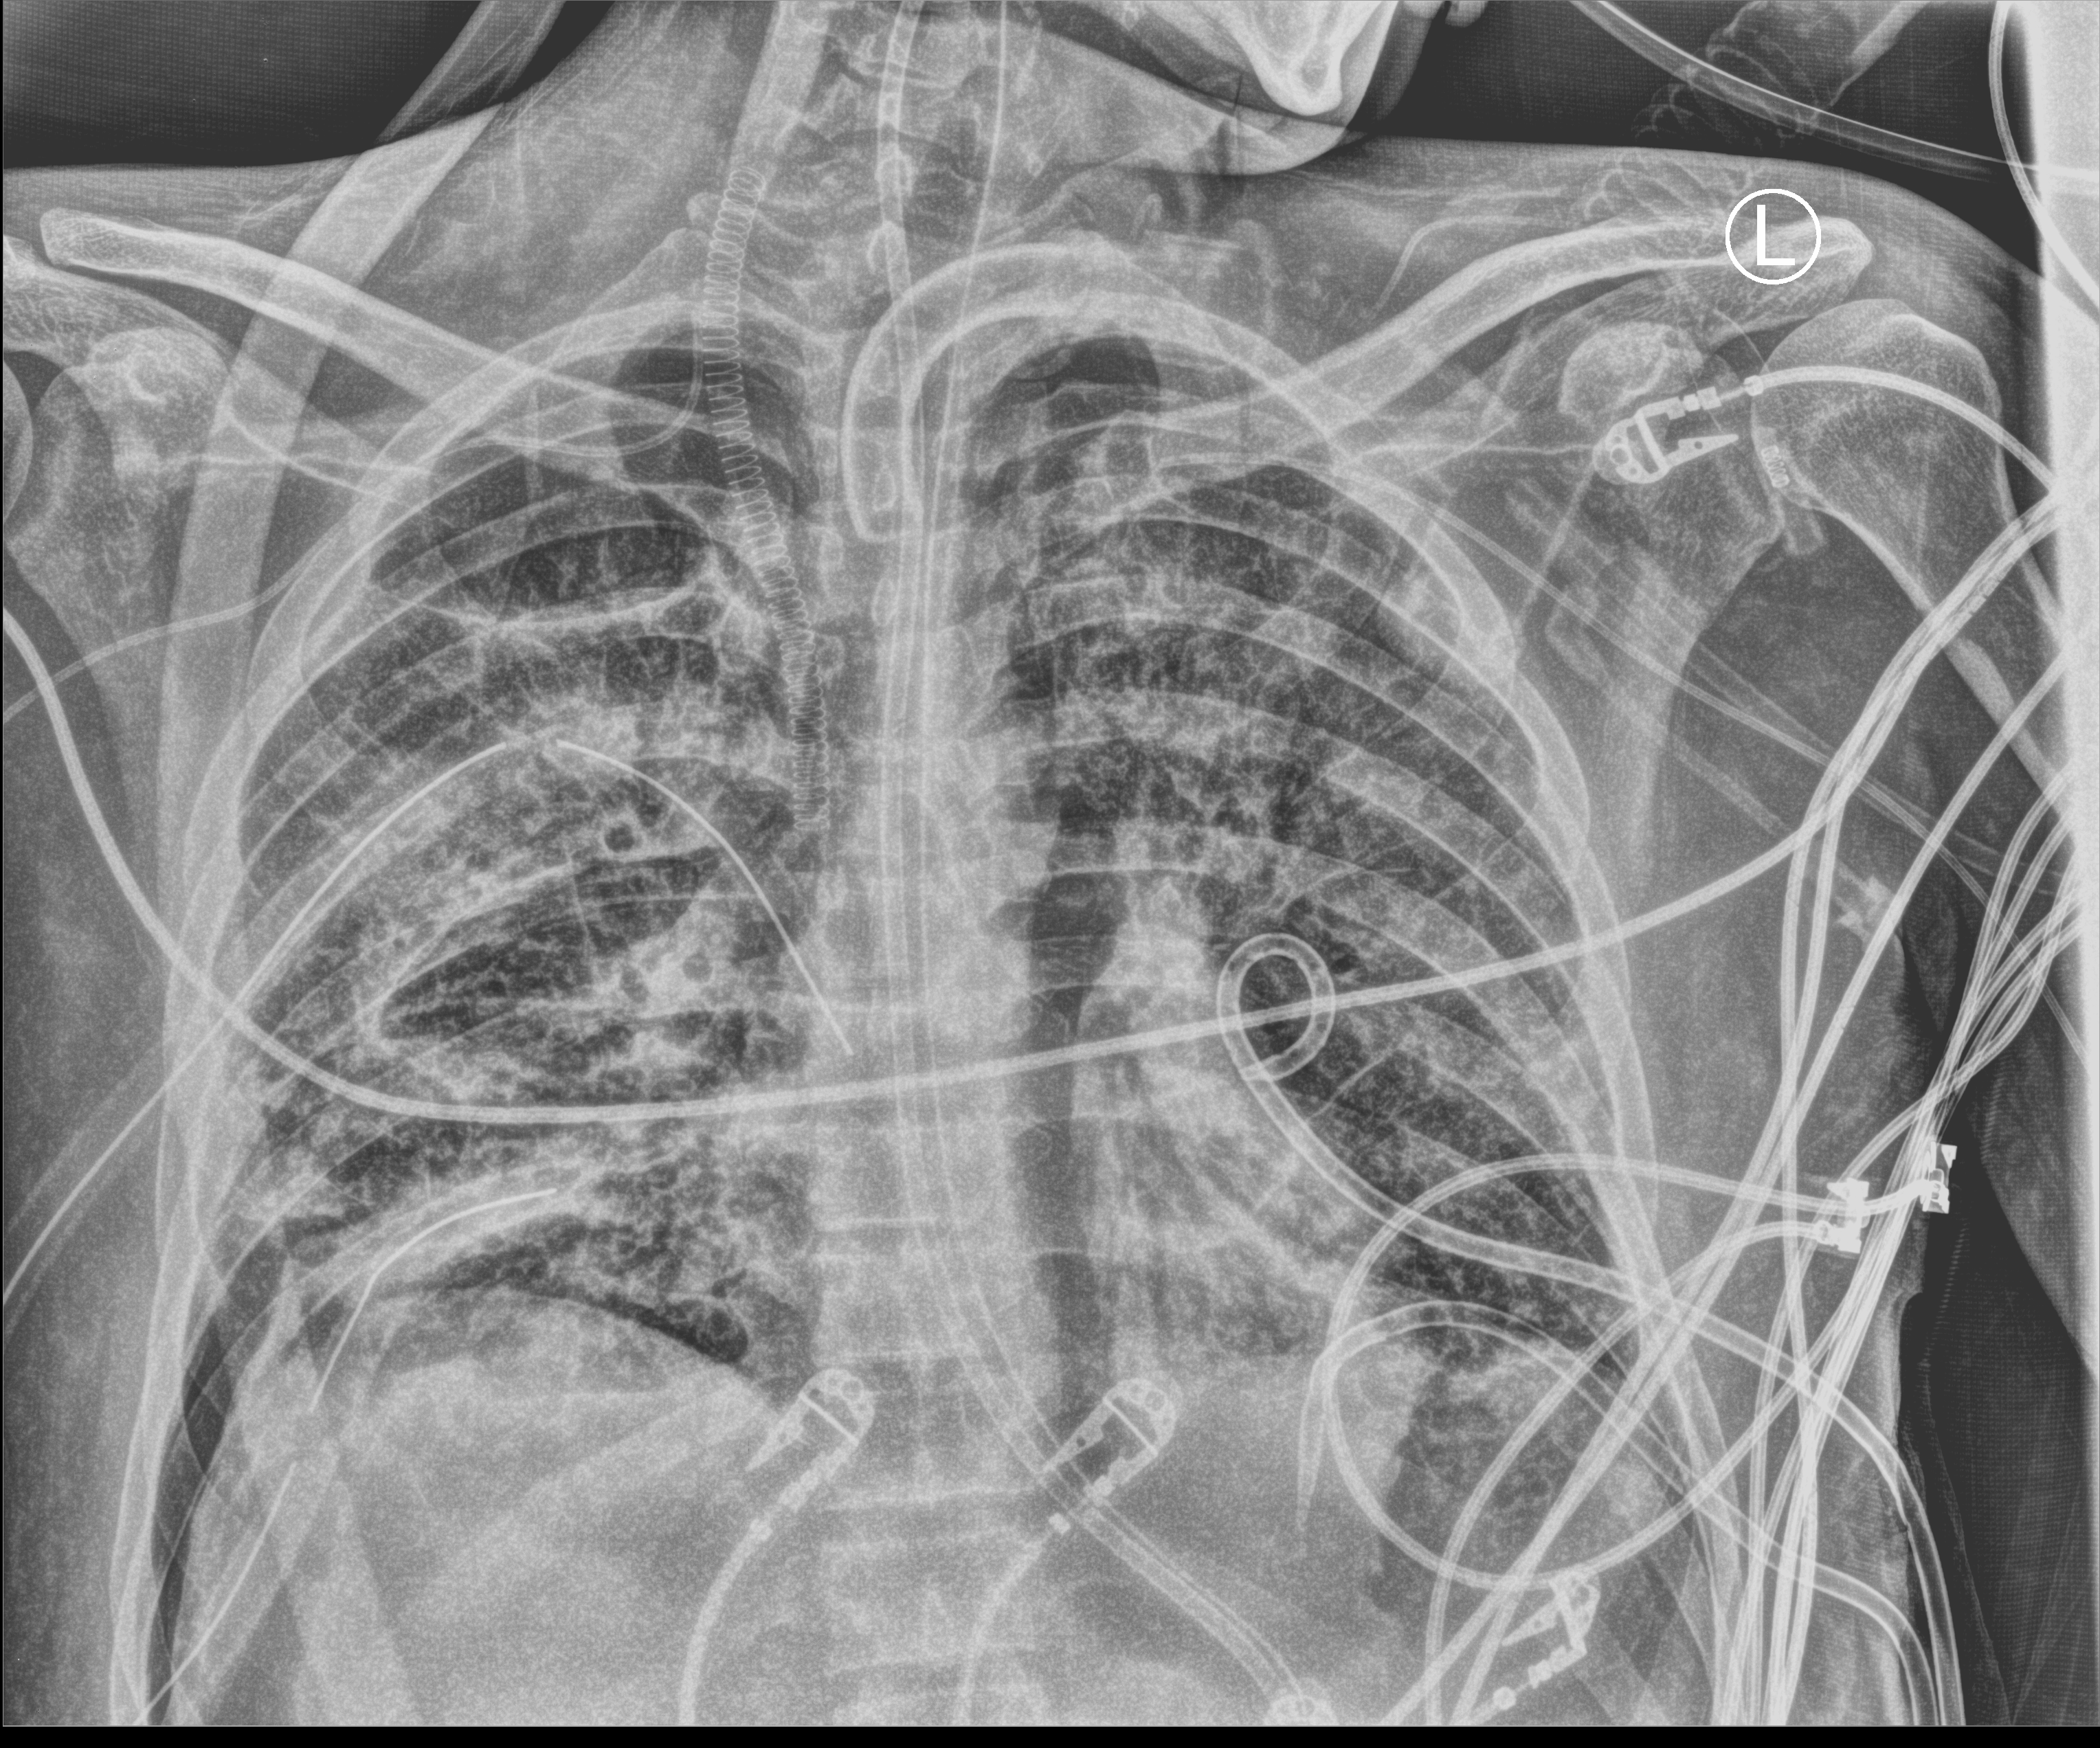
Bedside chest radiograph (computed radiography); anteroposterior (AP) projection. Adult patient hospitalised with COVID-19, age 18–59 years.
From the hospital-stay record, not from the radiograph (when in the stay this image was taken is not recorded): admitted to intensive care during this hospital stay: yes.